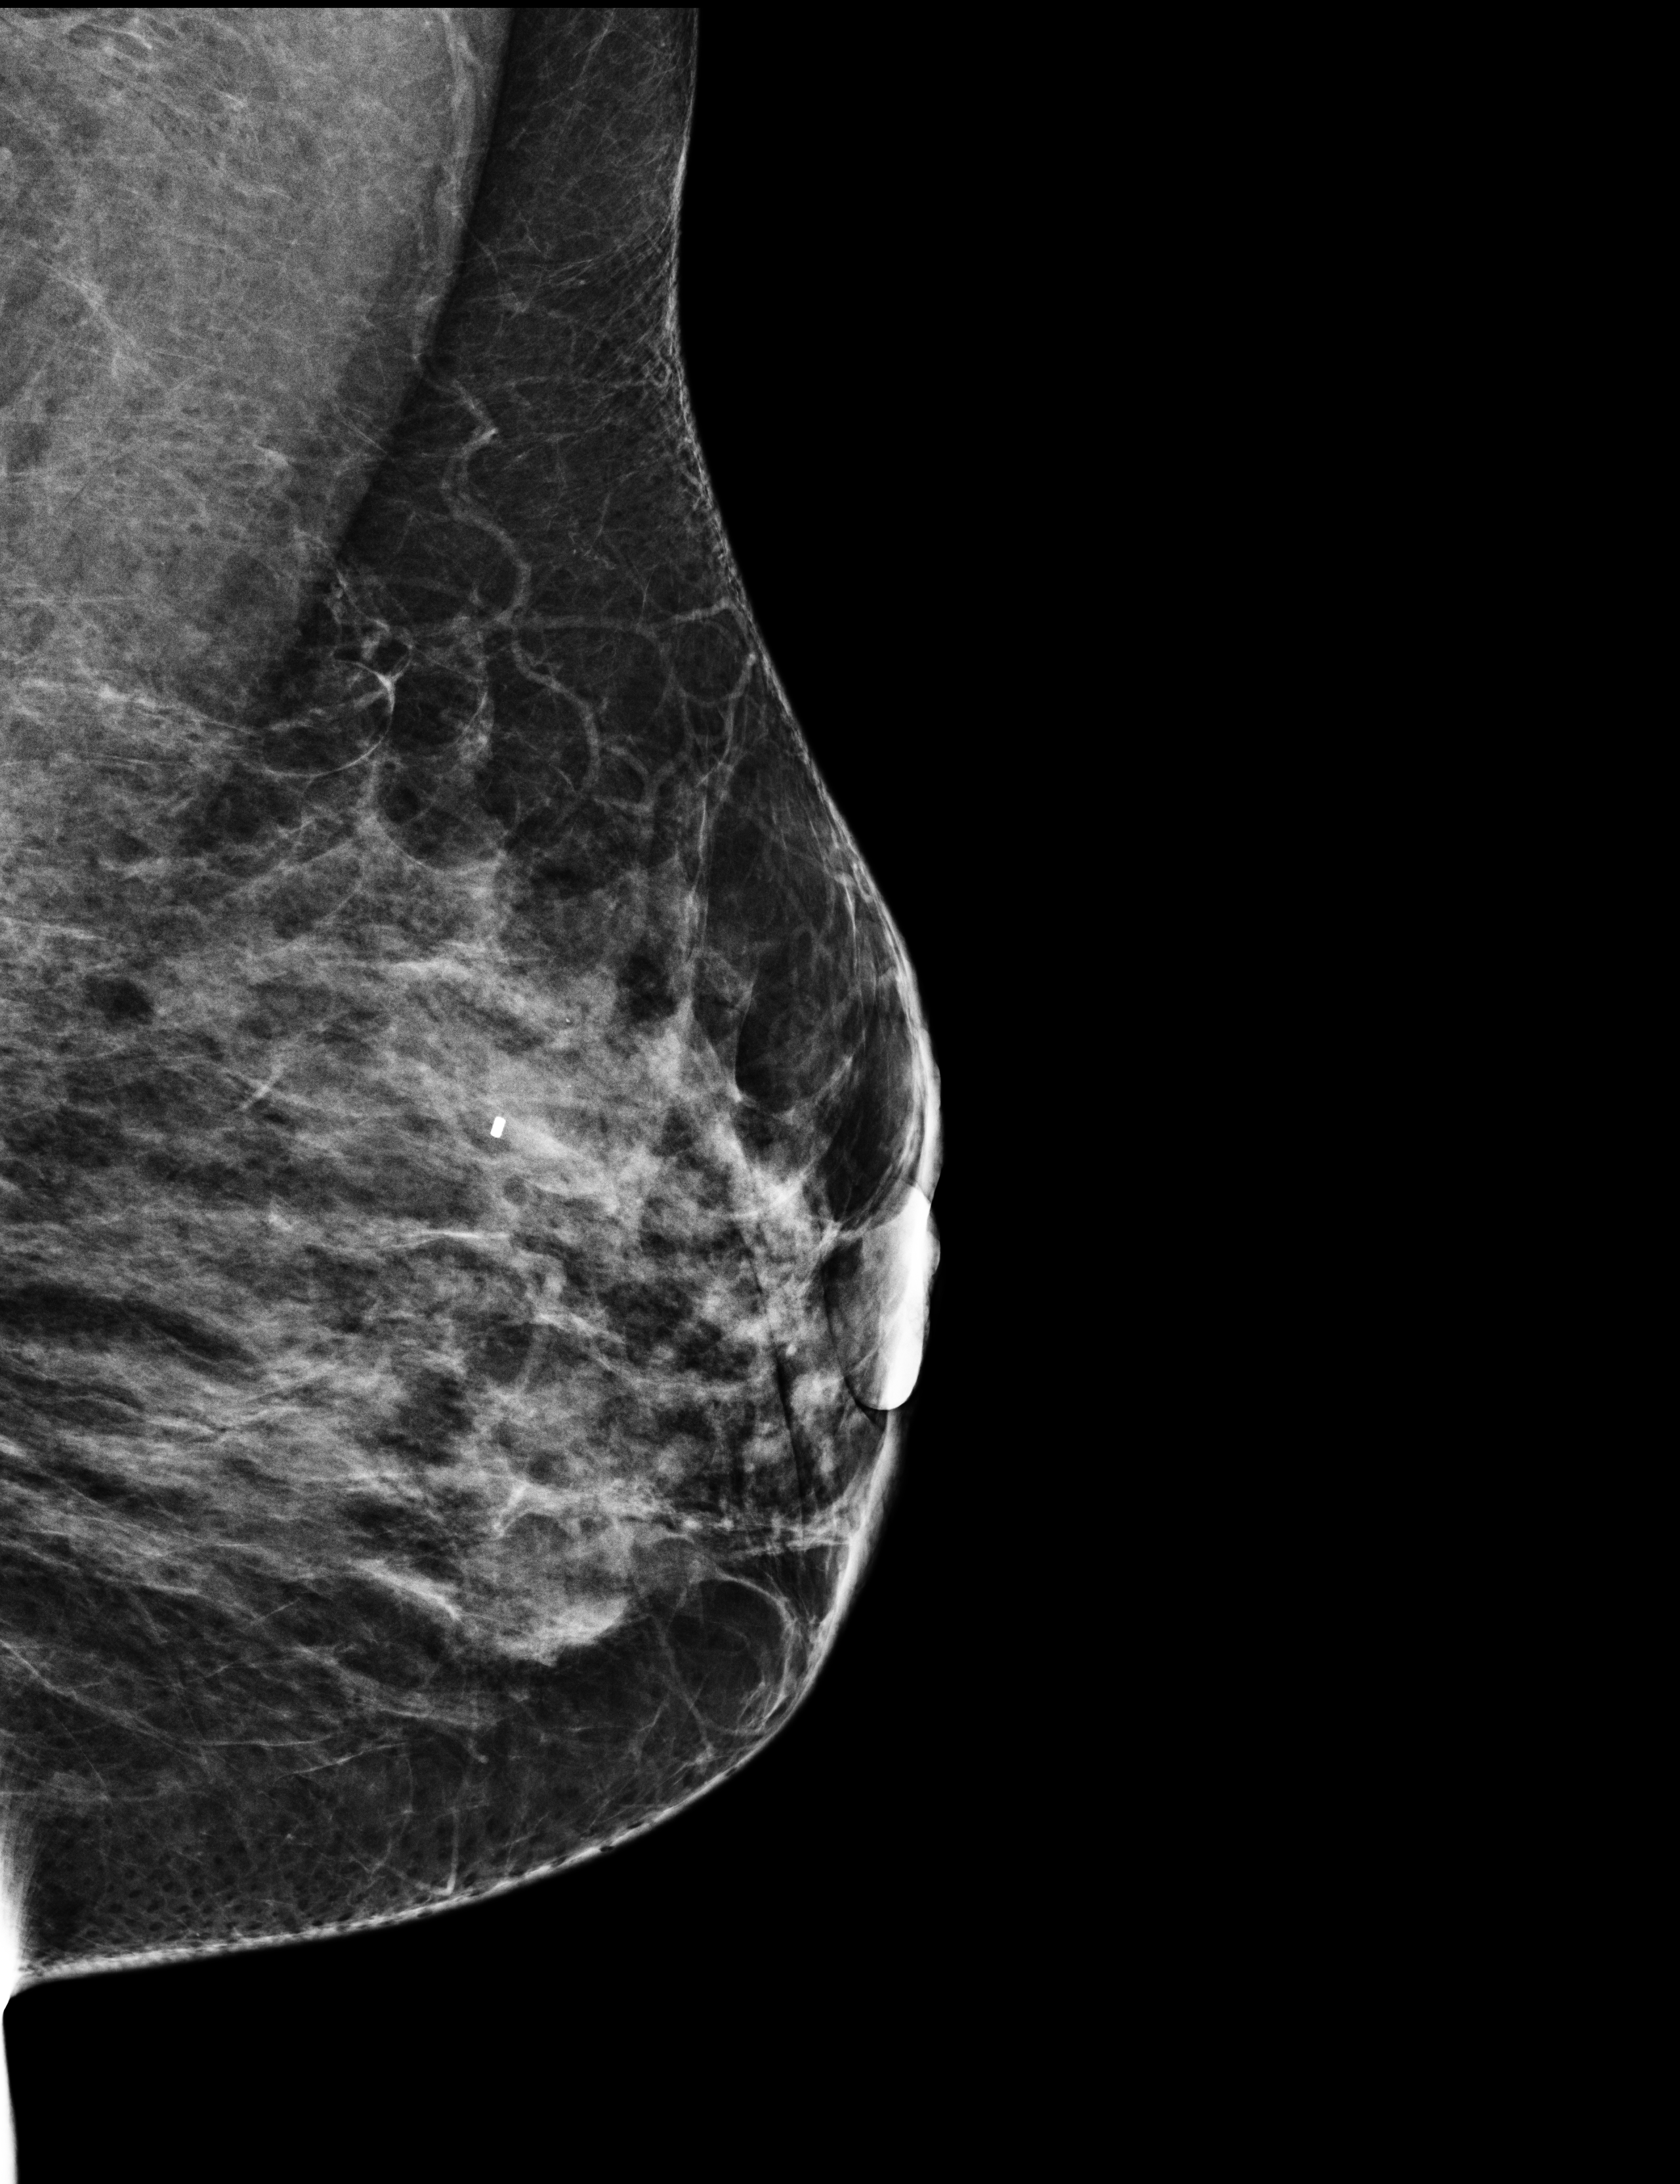
Digital mammogram (FFDM); left breast; mediolateral oblique (MLO) view; screening examination. Patient aged 42 years (female).
BI-RADS breast density category at the screening exam (both breasts, scale 1–4): 3. Final BI-RADS category for the screening round (tomosynthesis exam, both breasts): category 1. Recall: no recall after this screen.